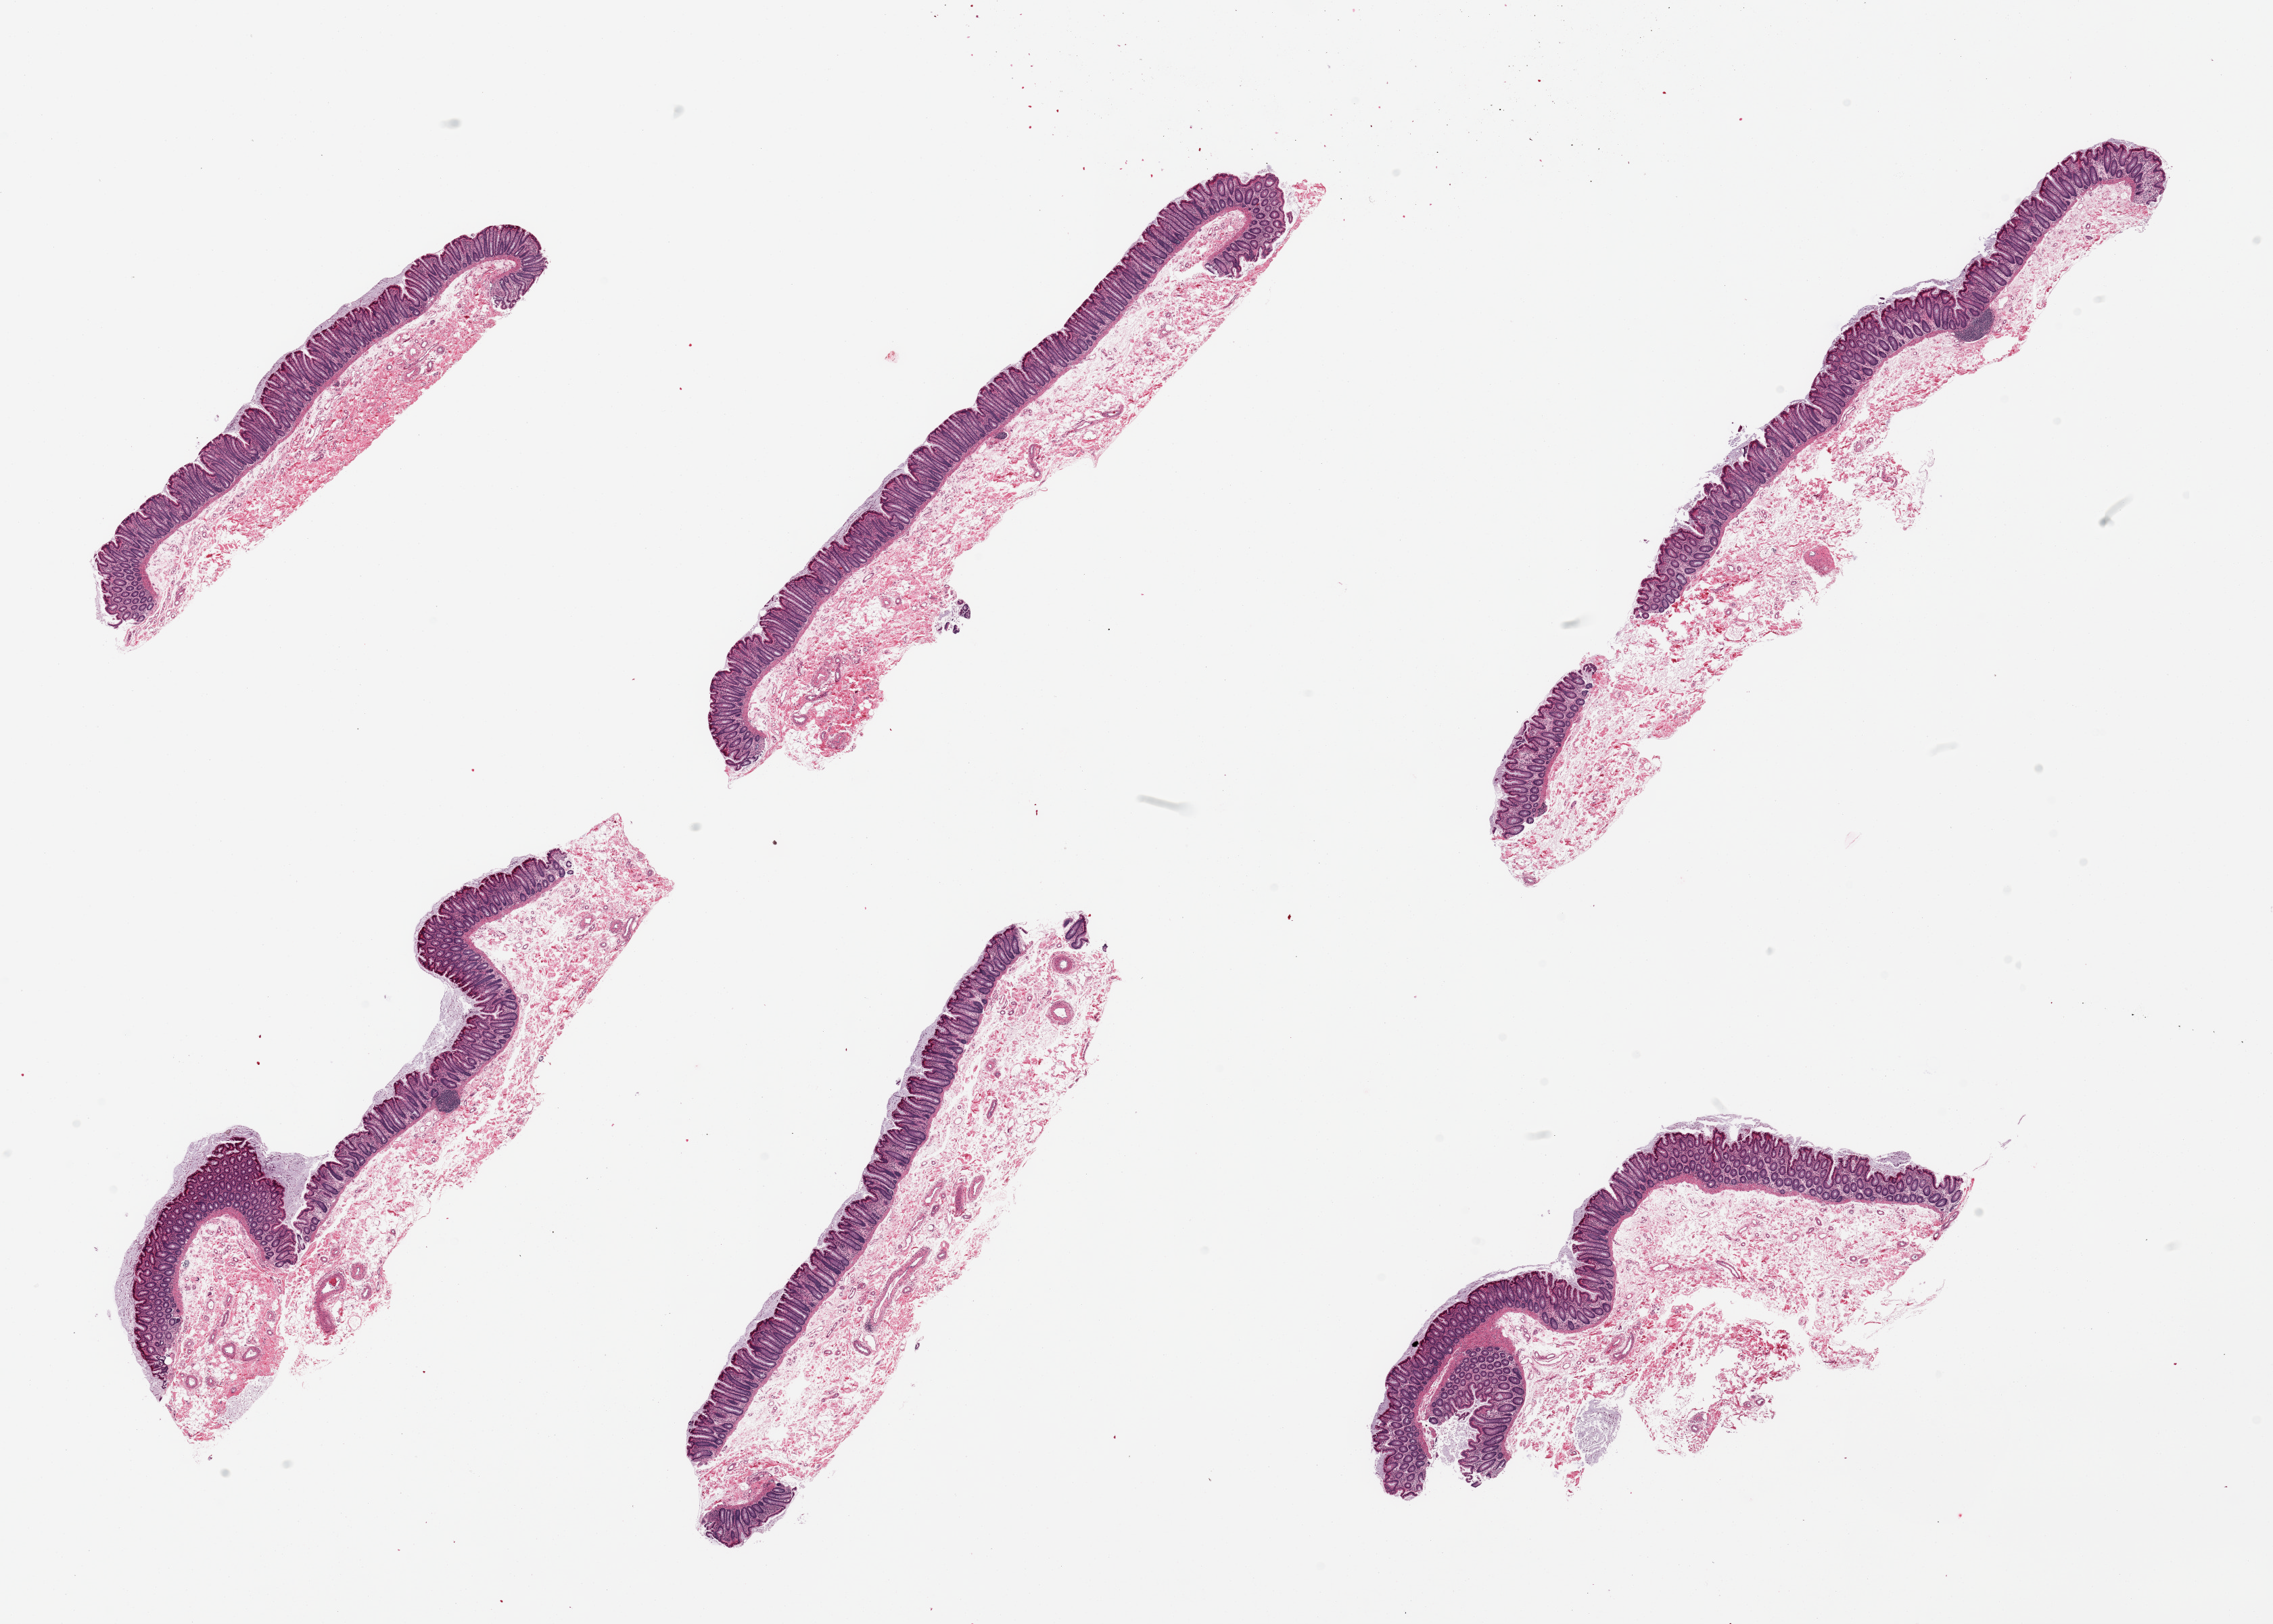
Whole-slide image, hematoxylin and eosin (H&E) stain, whole scanned area (about 26.6 x 19.0 mm, slide scanned at 20x) shown as a low-resolution overview. PAXgene-fixed, paraffin-embedded tissue. Sampled site (target tissue): transverse colon. Tissue donor sample. Female donor.
Pathologist's review note for this sample: 6 pieces, up to ~0.5mm, ~30% thickness.